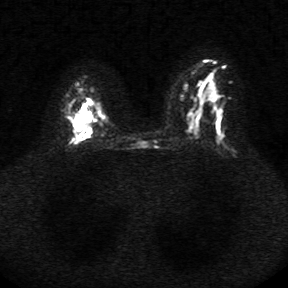
Breast MRI, one axial slice; position 20 of 34 along the scan axis; diffusion-weighted series; image 2 of 4 stored at this slice position (different b-values; order by instance number); 1.5 T; 5 mm slice thickness; 288 × 288 image matrix, field of view 340 × 340 mm. Female patient.
Annotated regions visible in this slice (manually delineated by an expert):
- tumour on diffusion-weighted imaging: box from (x=71, y=112) to (x=93, y=132) px